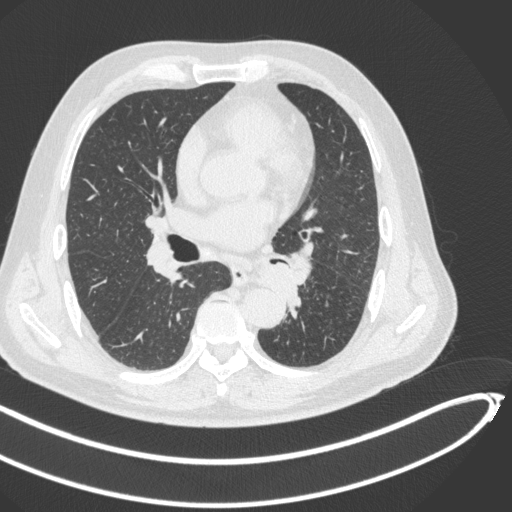
Chest CT, one axial slice. Position 246 of 466 along the scan axis. 120 kVp. Lung window (W 1500 / L -600 HU). 1 mm slice thickness. 512 × 512 image matrix, field of view 400 × 400 mm. Male patient, age 64 years. From the clinical record (not read from this slice): clinical TNM (as recorded): T1c N0 M0.
Structures marked on this image (rectangle marked by the reading radiologist):
- lung tumour (recorded histology: squamous cell carcinoma): bounding box (x1, y1, x2, y2) in pixels: (254, 257, 304, 310)